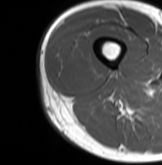
MRI of an extremity soft-tissue mass, one axial slice; slice 18 of 61 in the series (ordered by position); MR volume resampled by the dataset authors to the PET/CT grid (not the native acquisition matrix); 3.27 mm slice thickness; 162 × 165 image matrix, field of view 158 × 161 mm. Male patient. From the clinical record (not read from this slice): histological type: poorly differentiated synovial sarcoma; grade: high; site of the primary tumour: right buttock.
Annotated regions visible in this slice (expert contour drawn on MRI and transferred to this co-registered scan by the dataset authors):
- gross tumour volume including surrounding oedema: box from (x=57, y=45) to (x=99, y=87) px